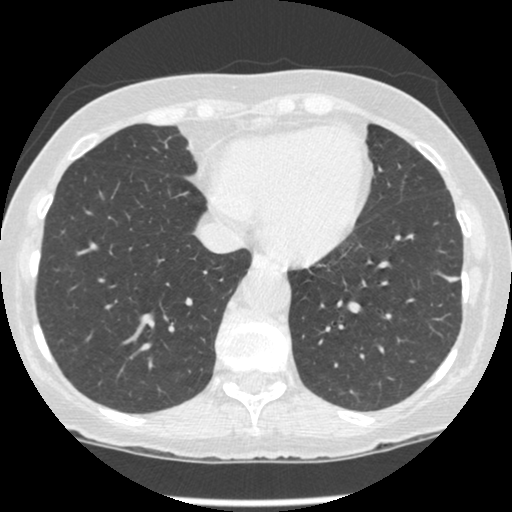
Low-dose screening chest CT, one axial slice; position 74 of 247 along the scan axis; 120 kVp; lung window (W 1500 / L -600 HU); 512 × 512 image matrix, field of view 303 × 303 mm.
Annotated regions visible in this slice (manually delineated by an expert):
- lesion 1 (tumor, lower lobe of left lung): box from (x=445, y=276) to (x=459, y=282) px